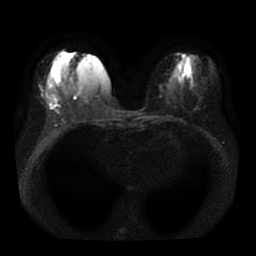
Breast MRI, one axial slice; position 17 of 41 along the scan axis; diffusion-weighted series; image 2 of 4 stored at this slice position (different b-values; order by instance number); 1.5 T; 5 mm slice thickness; 256 × 256 image matrix, field of view 330 × 330 mm. Female patient.
Outlined on this slice (manually delineated by an expert):
- tumour on diffusion-weighted imaging: bounding box [x1, y1, x2, y2] px = [47, 94, 58, 104]